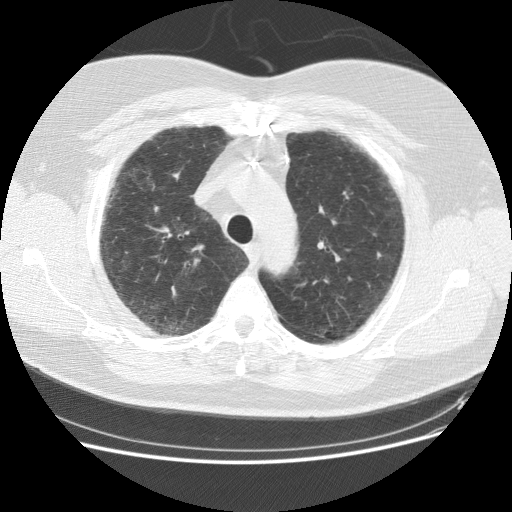
Low-dose screening chest CT, axial slice; baseline annual screen; lung window (W 1500 / L -600 HU); standard (soft-tissue) reconstruction kernel (STANDARD); 120 kVp; slice 31 of 151 in the series; 512 × 512 image matrix, field of view 378 × 378 mm. Male, age 59 years at enrolment.
Lesion marked by an expert reader, bounding box [x1, y1, x2, y2] px = [92, 166, 142, 225]. The screening reader recorded 2 non-calcified nodules or masses ≥4 mm on this exam (right middle lobe, right lower lobe); which of them this box marks is not recorded. Official screen result: positive, change unspecified: nodule(s) >= 4 mm or enlarging nodule(s), mass(es), or other non-specific abnormalities suspicious for lung cancer. Lung cancer was diagnosed 338 days after this screen: adenocarcinoma, NOS, right upper lobe, right middle lobe, moderately differentiated (G2), stage IA (AJCC 6th edition), 13 mm at pathology.